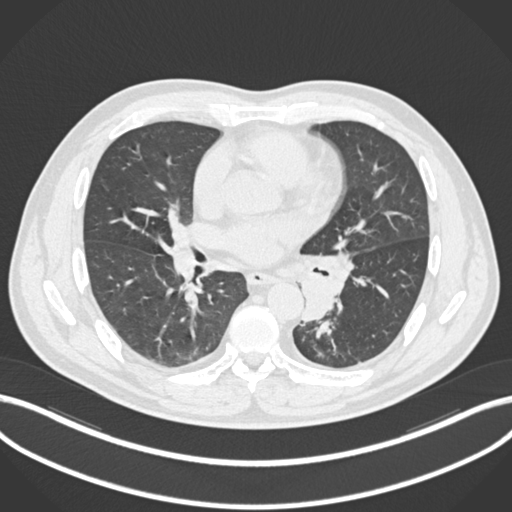
Chest CT, one axial slice; slice 112 of 223 in the series (ordered by position); reconstruction kernel B30f; lung window (W 1500 / L -600 HU); 1 mm slice thickness; 512 × 512 image matrix. Patient: male, 50 years. Case-level facts recorded for this patient, not image findings: clinical TNM (as recorded): T2a N3 M0.
Structures marked on this image (bounding box drawn by a radiologist):
- lung tumour (recorded histology: squamous cell carcinoma): bounding box <294,264,341,327> (left, top, right, bottom; pixels)